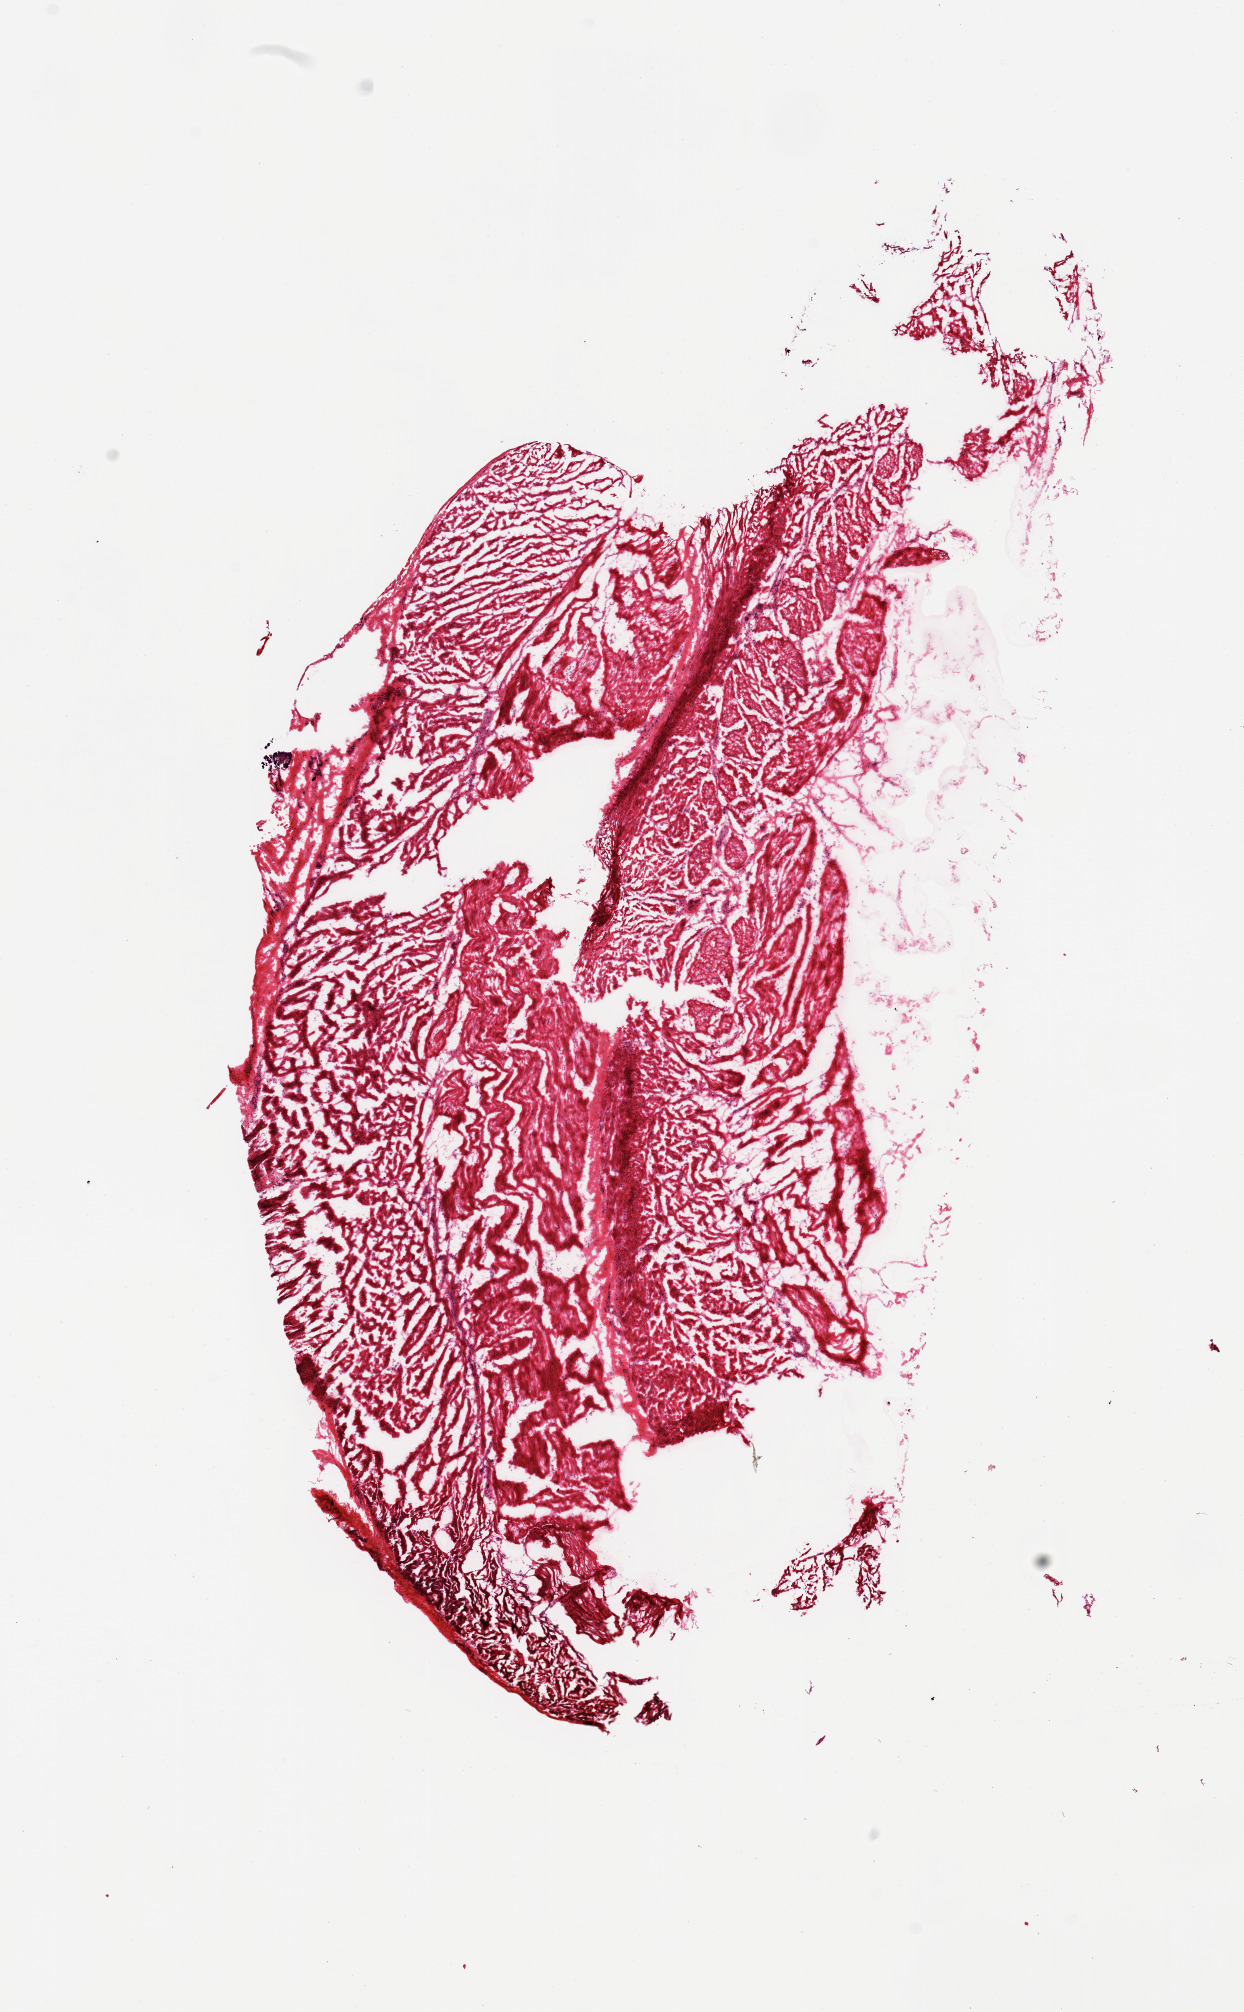
H&E whole-slide image — low-resolution overview of the scanned area, about 9.8 x 15.9 mm; frozen section; sampled site (target tissue): esophageal muscle; tissue donor sample.
Reviewer comment on this tissue sample: 1 piece; muscularis.